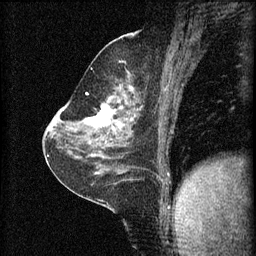
Breast MRI (dynamic contrast-enhanced), one sagittal slice. Slice 33 of 60 in the series (ordered by position). 3 images stored at this slice position (order not interpretable as contrast timing). 1.5 T. TE 4.2 ms, TR 8.2 ms. 2 mm slice thickness. 256 × 256 image matrix. Patient: female, 59 years.
Annotated regions visible in this slice (semi-automatic segmentation, software-assisted and operator-edited):
- analysis volume of interest (the breast-tissue region the enhancement analysis was run in; not a lesion): bounding box <78,92,137,135> (left, top, right, bottom; pixels)
- tumour enhancement mask (voxels above the 70 % enhancement threshold inside the analysis volume of interest): <84,104,133,129>